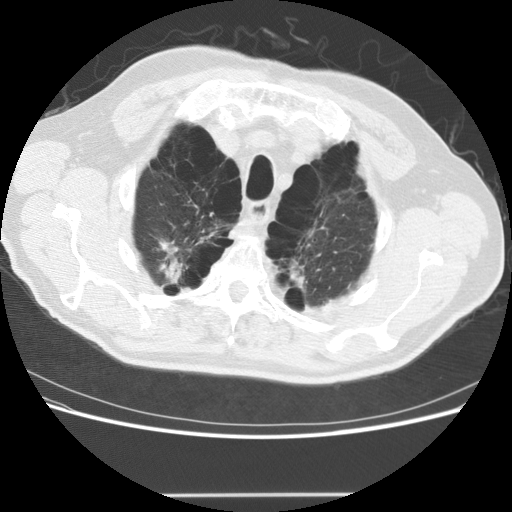
Low-dose screening chest CT, axial slice. Third annual screen. Lung window (W 1500 / L -600 HU). 2.5 mm slice thickness. Male participant, aged 68 years at enrolment.
Lesion marked by an expert reader, box from (x=129, y=216) to (x=215, y=296) px. The screening reader recorded 2 non-calcified nodules or masses ≥4 mm on this exam (lingula, left lower lobe); which of them this box marks is not recorded.